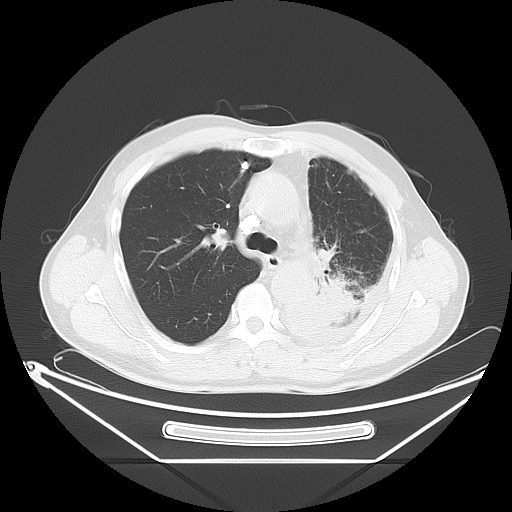
Chest CT, one axial slice; slice 42 of 63 in the series (ordered by position); reconstruction kernel LUNG; 120 kVp; lung window (W 1500 / L -600 HU); 5 mm slice thickness; 512 × 512 image matrix. Patient: male, 60 years. Case-level facts recorded for this patient, not image findings: clinical TNM (as recorded): T4 N1 M1.
Structures marked on this image (rectangle marked by the reading radiologist):
- lung tumour (recorded histology: adenocarcinoma): box from (x=303, y=264) to (x=363, y=336) px